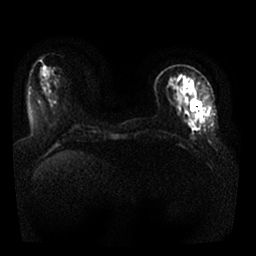
Breast MRI, one axial slice; slice 7 of 25 in the series (ordered by position); diffusion-weighted series; image 2 of 4 stored at this slice position (different b-values; order by instance number); 1.5 T; 256 × 256 image matrix, field of view 330 × 330 mm. Female patient.
Annotated regions visible in this slice (outlined manually by an expert reader):
- tumour on diffusion-weighted imaging: bounding box (x1, y1, x2, y2) in pixels: (191, 101, 202, 110)